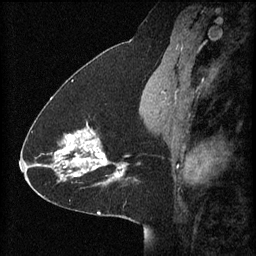
Breast MRI (dynamic contrast-enhanced), one sagittal slice; position 30 of 60 along the scan axis; 3 images stored at this slice position (order not interpretable as contrast timing); 1.5 T; TE 4.2 ms, TR 8.2 ms; 2 mm slice thickness; 256 × 256 image matrix, field of view 200 × 200 mm. Patient: female, 41 years.
Structures marked on this image (semi-automatically segmented with operator editing):
- analysis volume of interest (the breast-tissue region the enhancement analysis was run in; not a lesion): bounding box <58,122,128,181> (left, top, right, bottom; pixels)
- tumour enhancement mask (voxels above the 70 % enhancement threshold inside the analysis volume of interest): <58,124,126,181>